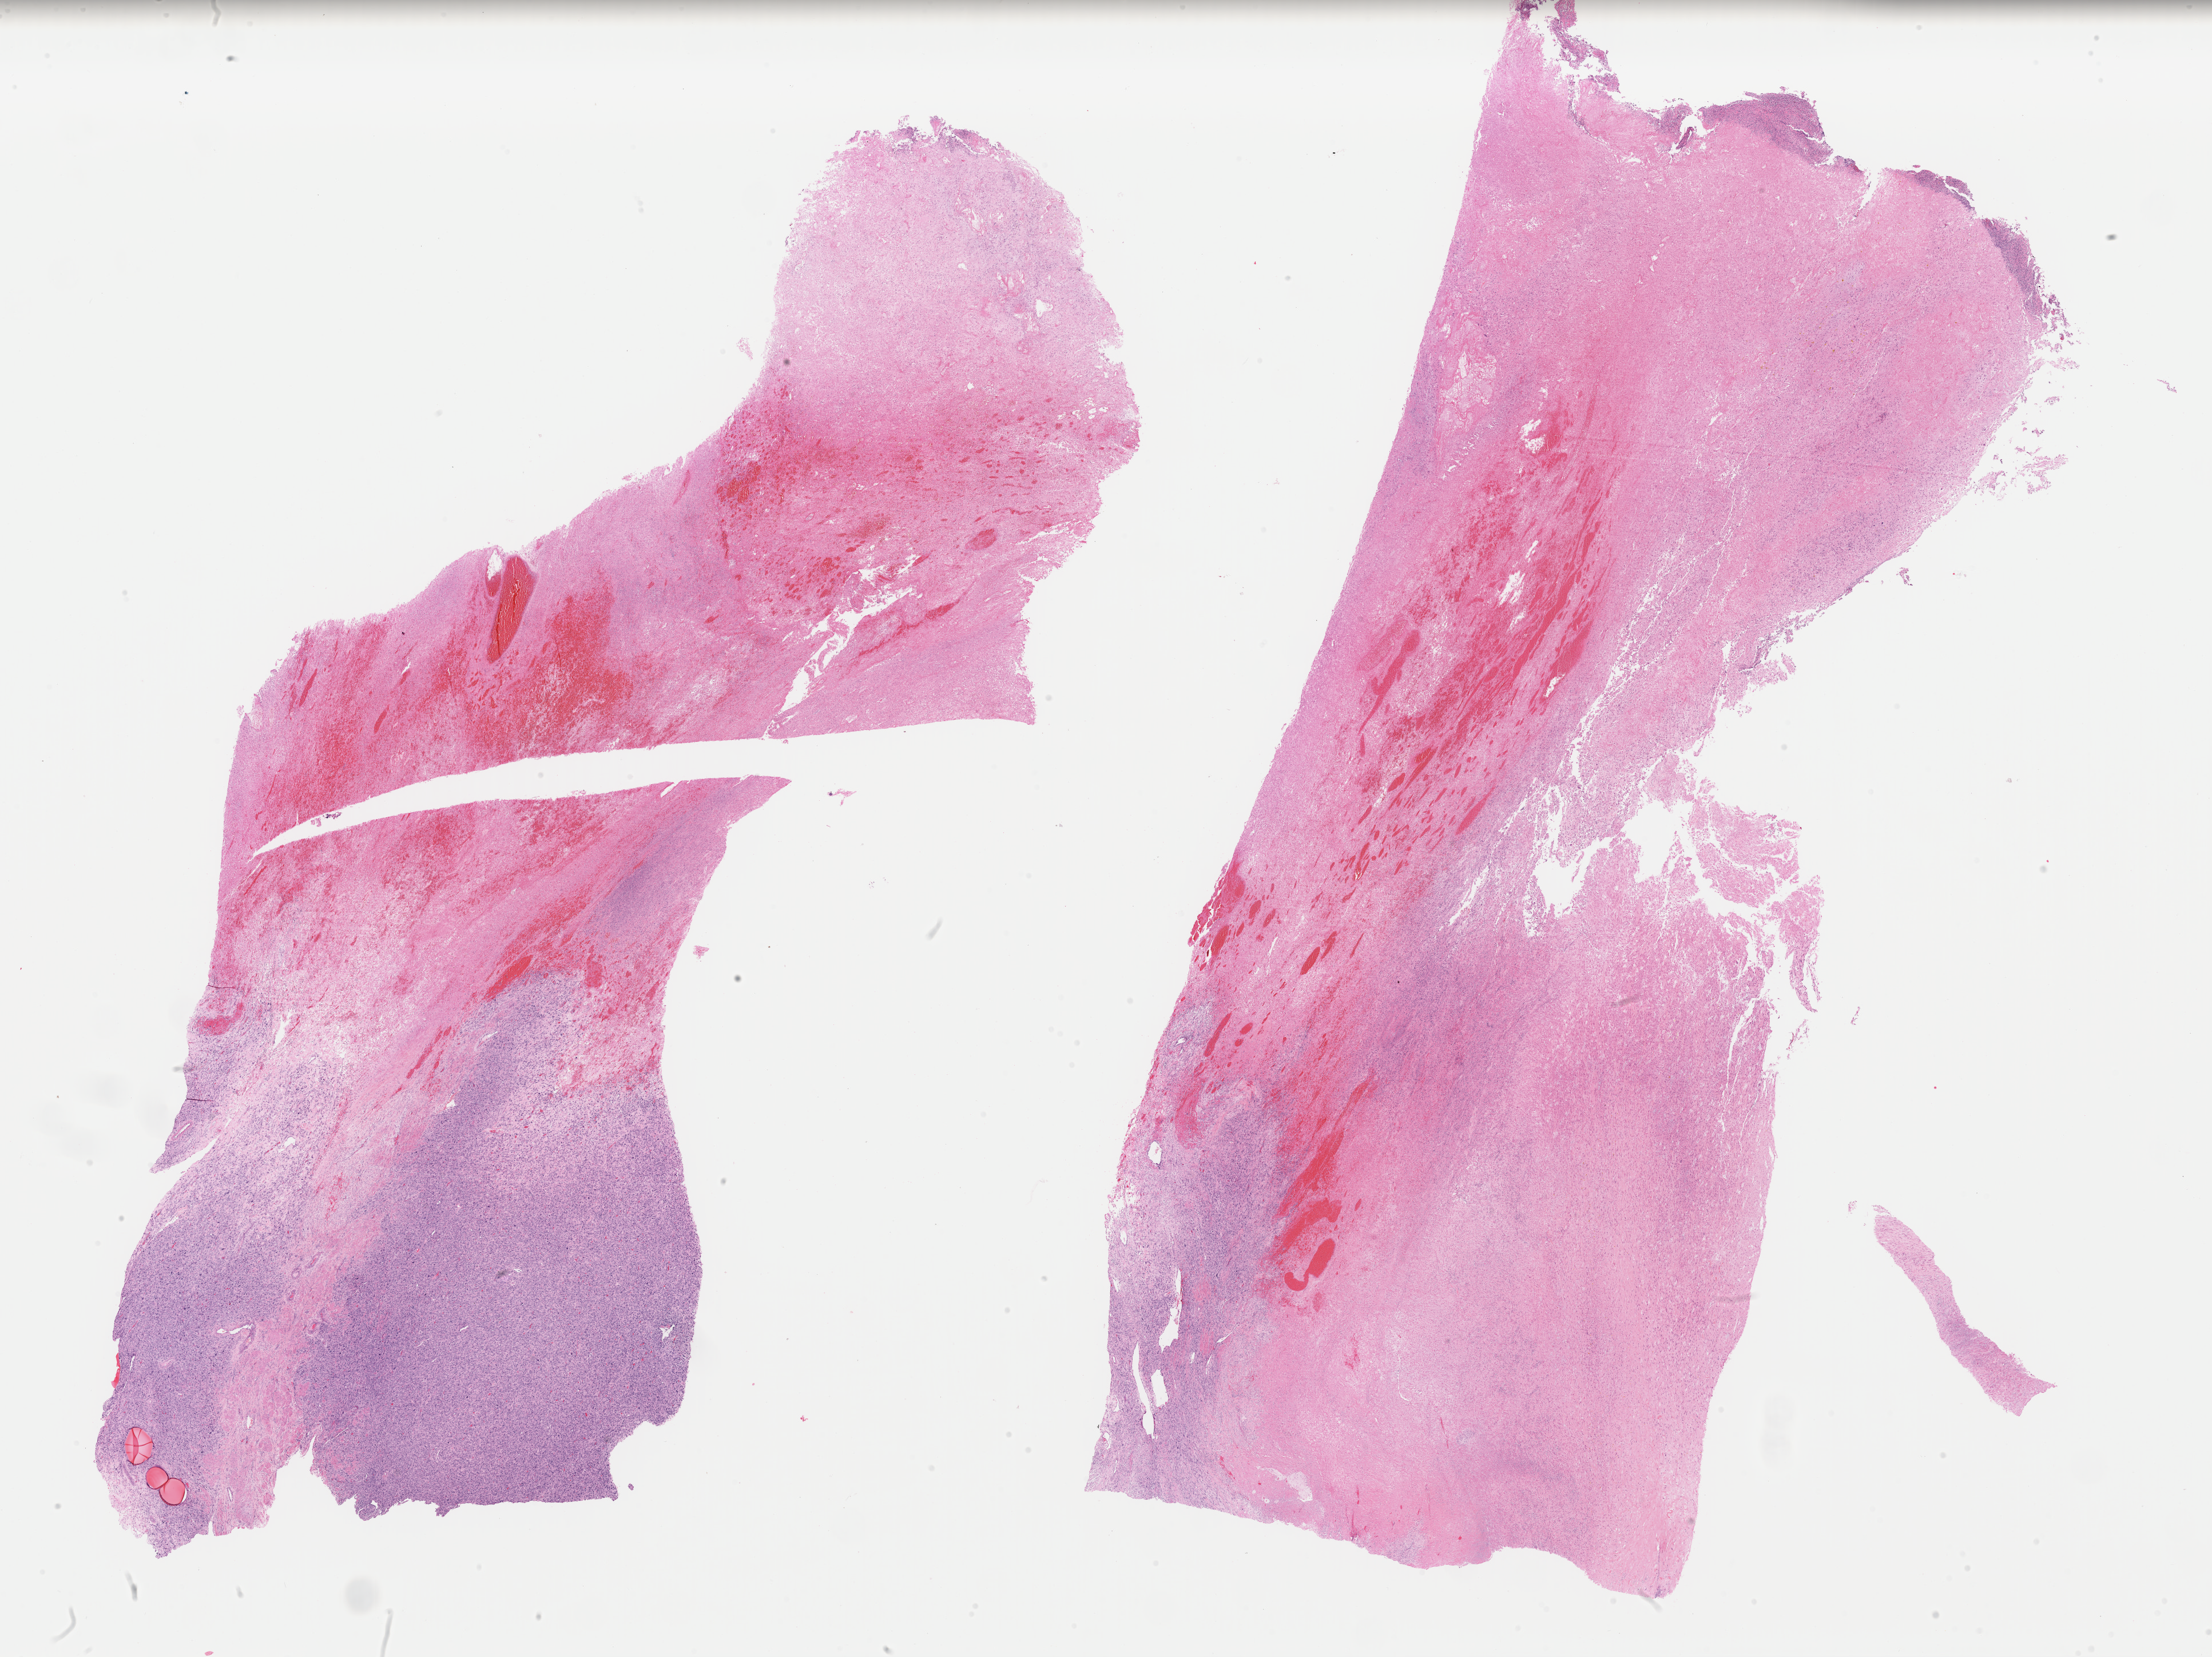
Digitized Hematoxylin and eosin (H&E) stained tissue section (whole slide) — a low-resolution overview of the entire scanned area, about 30.5 x 22.9 mm; FFPE section; primary tumour sample from the uterus. Female patient; age at initial diagnosis 41 years.
Histologic diagnosis: Leiomyosarcoma, NOS.